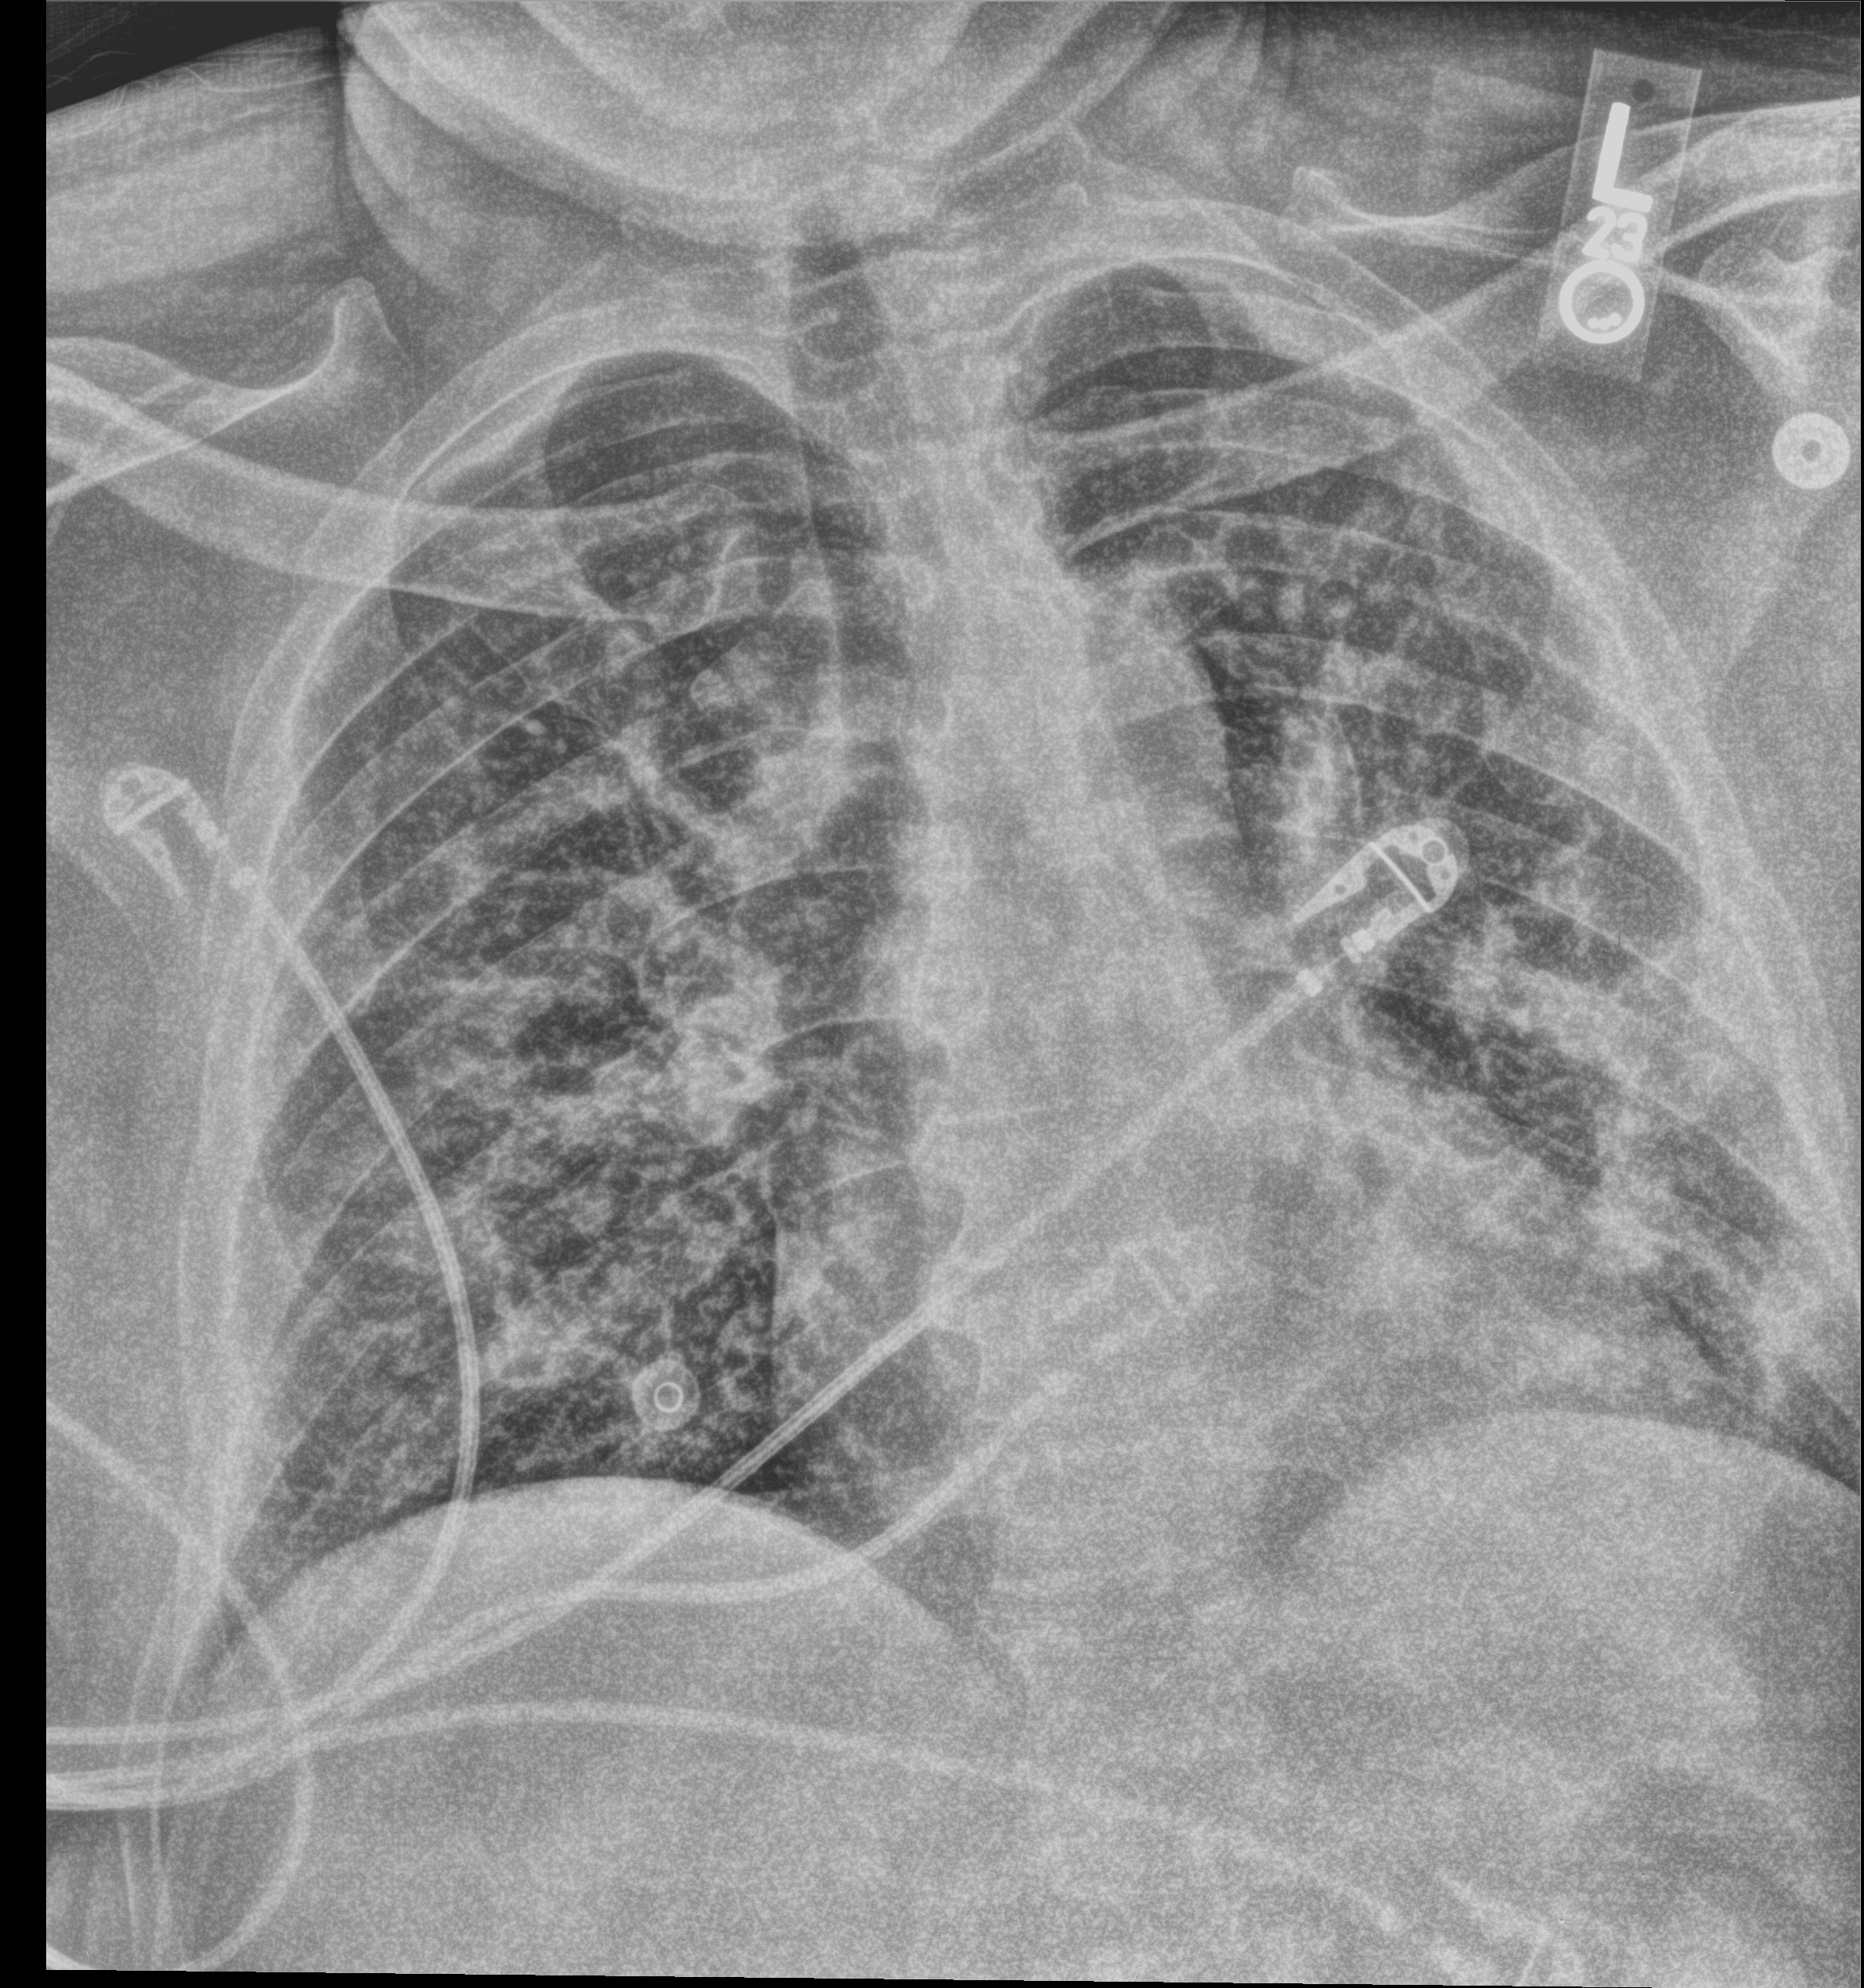
Bedside chest radiograph (computed radiography); anteroposterior (AP) projection. Patient hospitalised with COVID-19; male, aged 18–59 years.
From the hospital-stay record, not from the radiograph (when in the stay this image was taken is not recorded): admitted to intensive care during this hospital stay: yes; length of hospital stay: 15 days; mechanically ventilated during this hospital stay: yes.